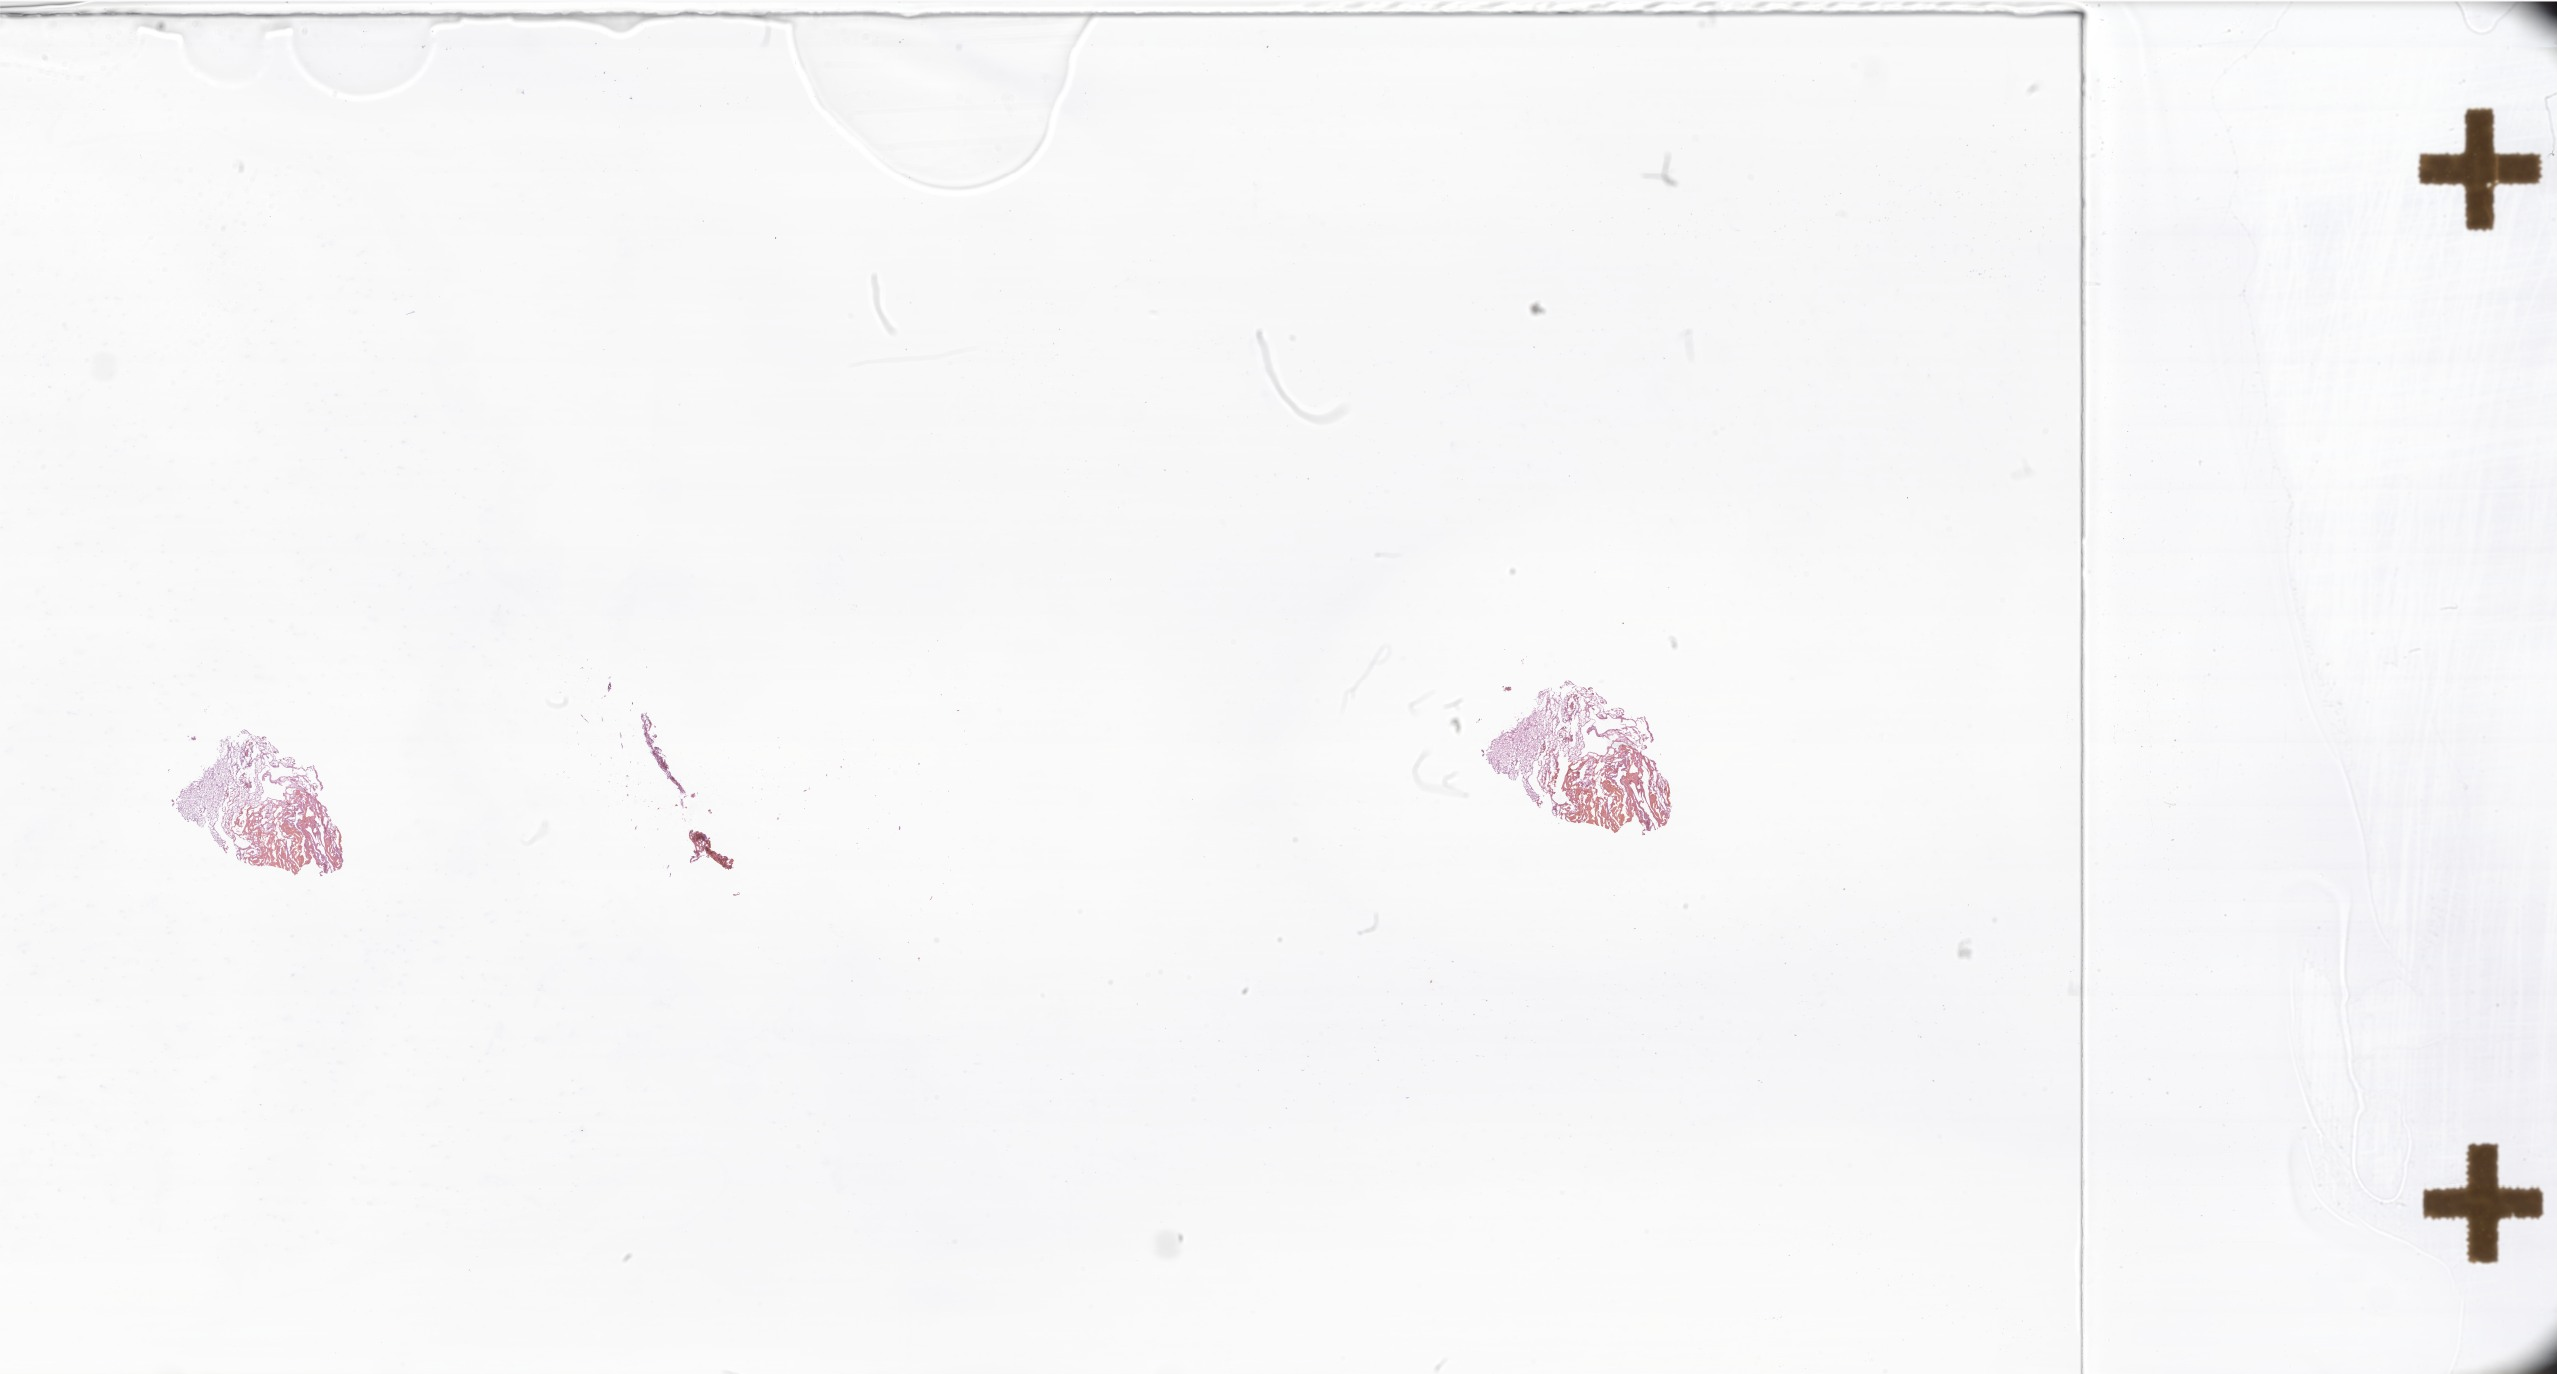
Whole-slide image, haematoxylin and eosin stain of tumor tissue from the brain — whole scanned area (about 43.1 x 23.2 mm) shown as a low-resolution overview; cryosection (OCT / tissue freezing medium). Patient: female, age 126 months (10 years 6 months).
- diagnosis: Pilocytic astrocytoma